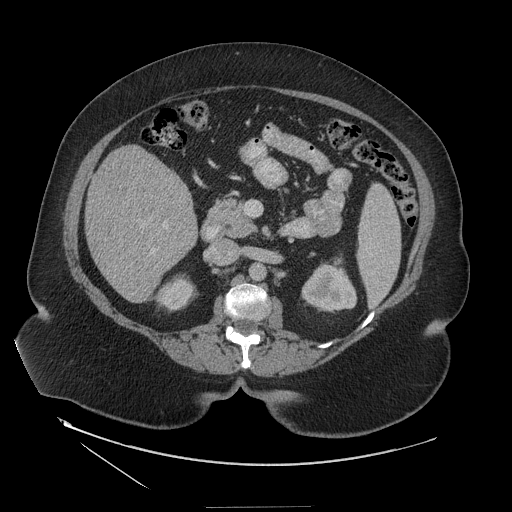
Contrast-enhanced abdominal CT (liver protocol), one axial slice; position 56 of 127 along the scan axis; reconstruction kernel STANDARD; 140 kVp; soft-tissue window (W 400 / L 40 HU); 512 × 512 image matrix, field of view 480 × 480 mm. Case-level facts recorded for this patient, not image findings: diagnosis: hepatocellular carcinoma (patient treated with transarterial chemoembolisation; whether this scan precedes or follows treatment is not stated here); TNM stage (as recorded): Stage-II; Child-Pugh class: A.
Structures marked on this image (semi-automatic segmentation, software-assisted and operator-edited):
- liver parenchyma outside the tumour (the mass and vessels are separate outlines, so this box may not span the whole liver): box from (x=86, y=146) to (x=198, y=302) px
- liver vessels: (x=151, y=225)–(x=166, y=253)